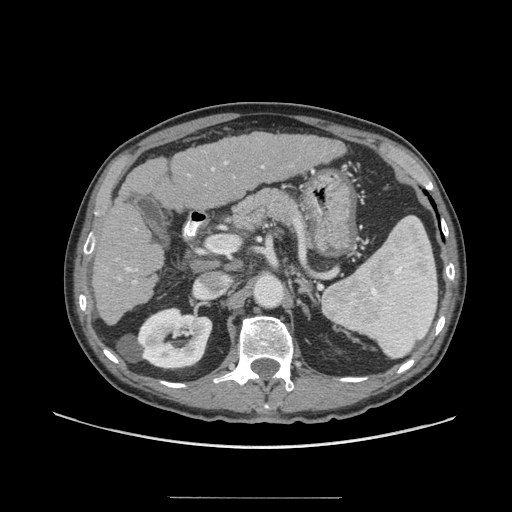
Contrast-enhanced abdominal CT (liver protocol), one axial slice. Position 34 of 71 along the scan axis. Reconstruction kernel STANDARD. Soft-tissue window (W 400 / L 40 HU). 2.5 mm slice thickness. 512 × 512 image matrix, field of view 400 × 400 mm. Case-level facts recorded for this patient, not image findings: diagnosis: hepatocellular carcinoma (patient treated with transarterial chemoembolisation; whether this scan precedes or follows treatment is not stated here); TNM stage (as recorded): Stage-I.
Outlined on this slice (semi-automatically segmented with operator editing):
- liver parenchyma outside the tumour (the mass and vessels are separate outlines, so this box may not span the whole liver): bounding box <92,132,344,324> (left, top, right, bottom; pixels)
- liver vessels: <117,161,265,284>